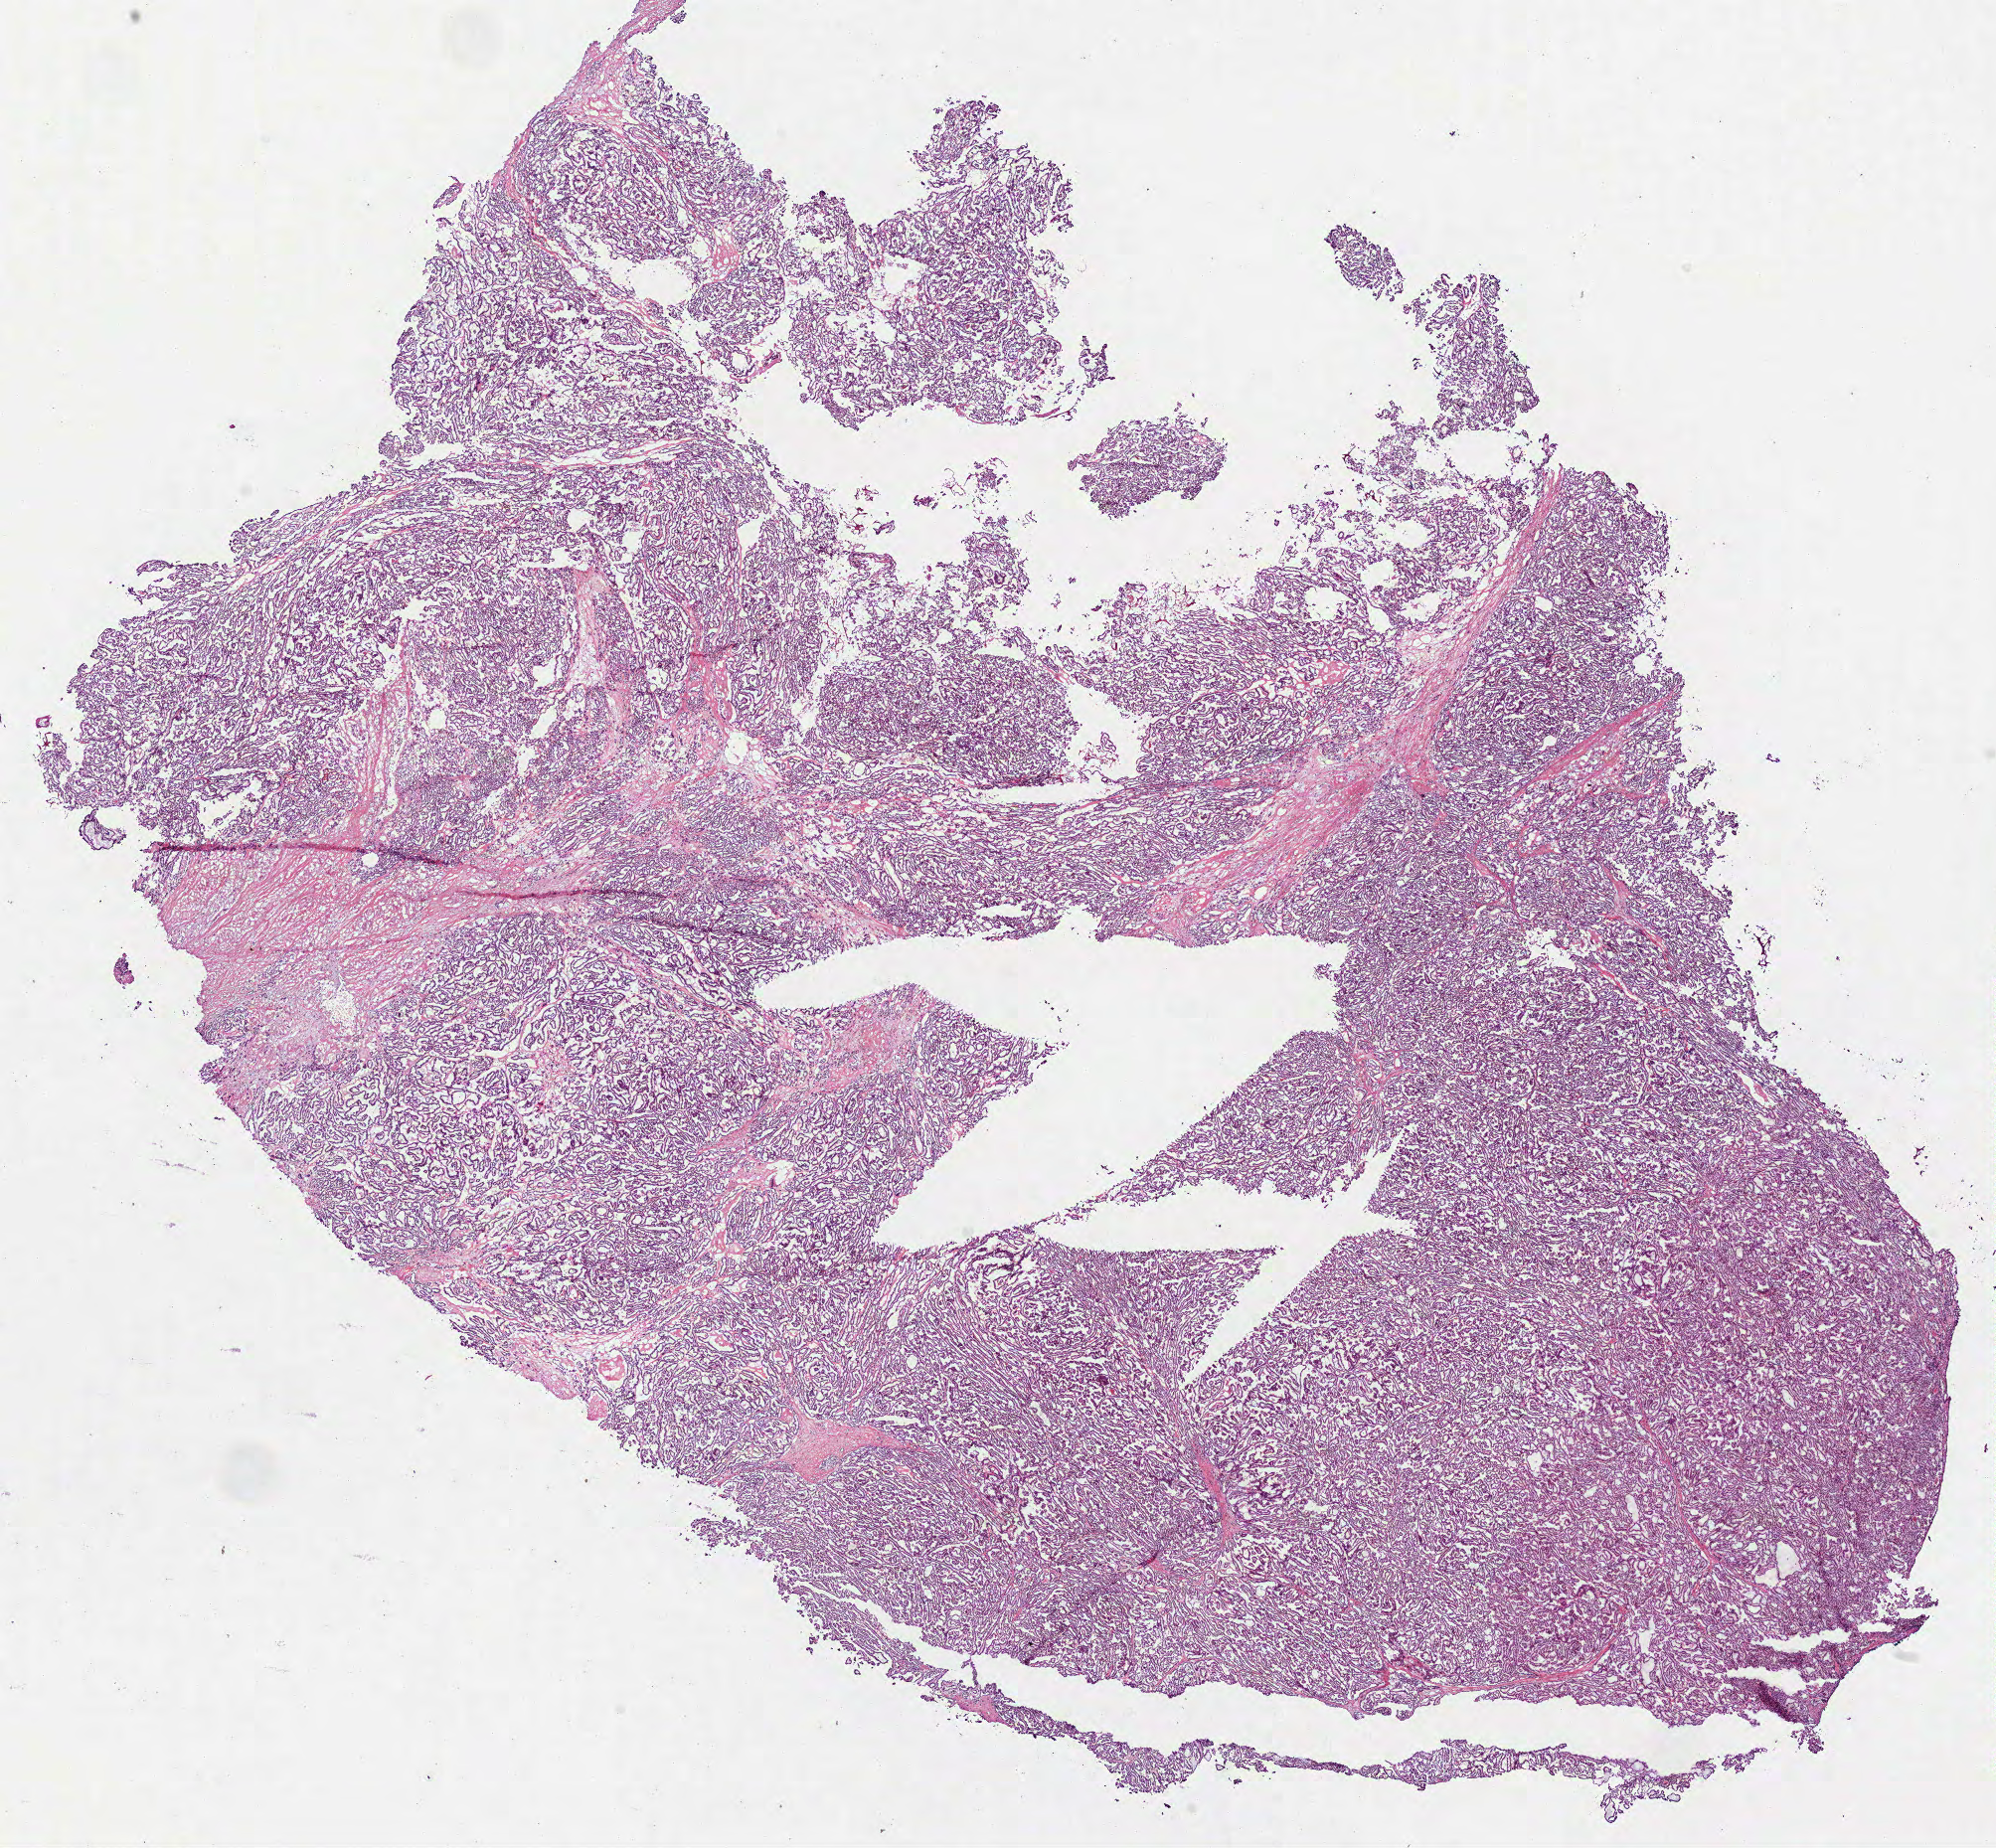
Whole-slide histology image, H&E-stained — low-resolution overview of the scanned area, about 16.2 x 15.0 mm (acquisition: 40x scan). Frozen section. Sample: primary tumour, kidney. Patient: female, age at initial diagnosis 58 years. Pathologist review of this section (percent, as recorded): tumour cells 95%, tumour nuclei 95%, normal cells 0%, stromal cells 5%, necrosis 0%.
* diagnosis: Papillary adenocarcinoma, NOS
* AJCC pathologic stage: I
* TNM: T1b NX MX